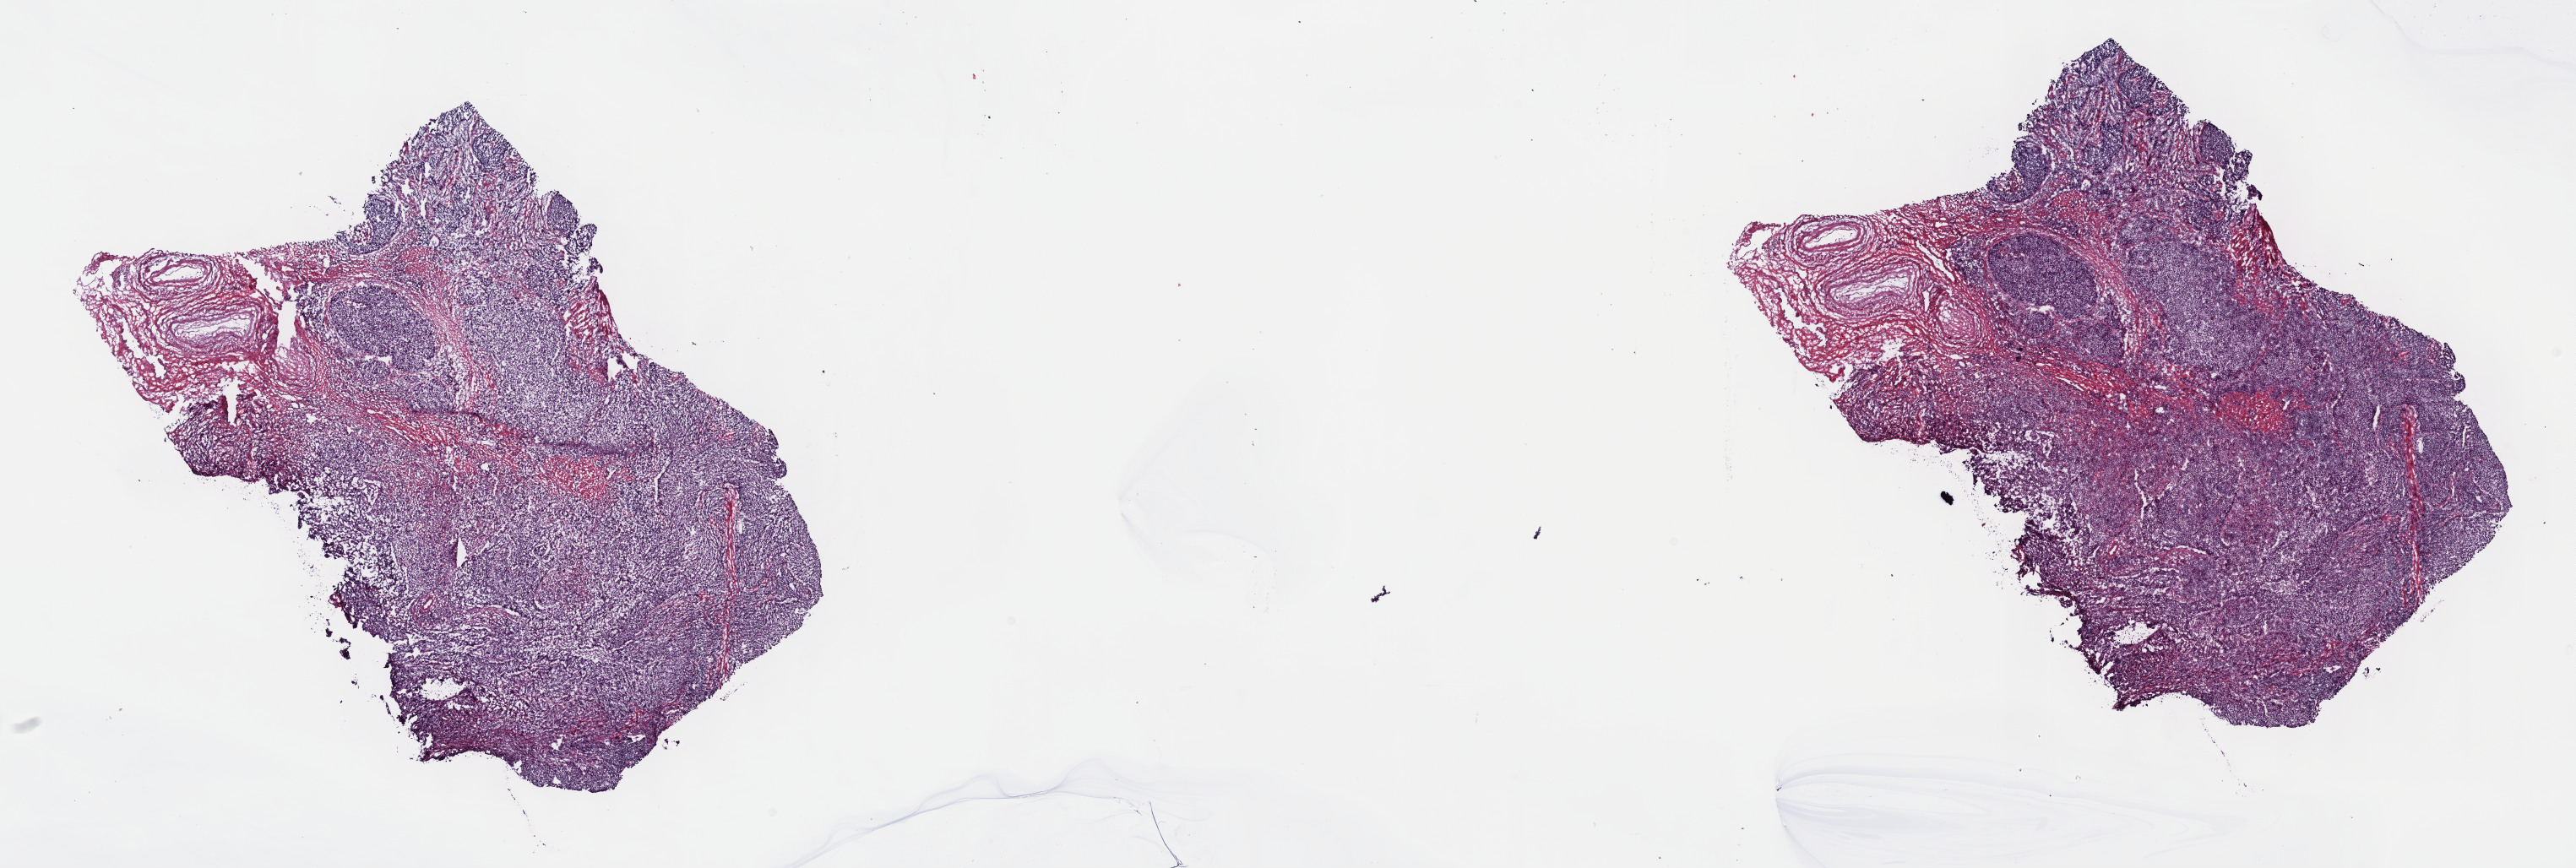
H&E whole-slide image, whole scanned area (about 24.7 x 8.3 mm) shown as a low-resolution overview; frozen section; cervix, primary tumour sample. Female, age 54 years at initial diagnosis. Composition of this section per pathologist review: tumour cells 70%, tumour nuclei 70%.
Diagnosis: Squamous cell carcinoma, NOS (cervix uteri).